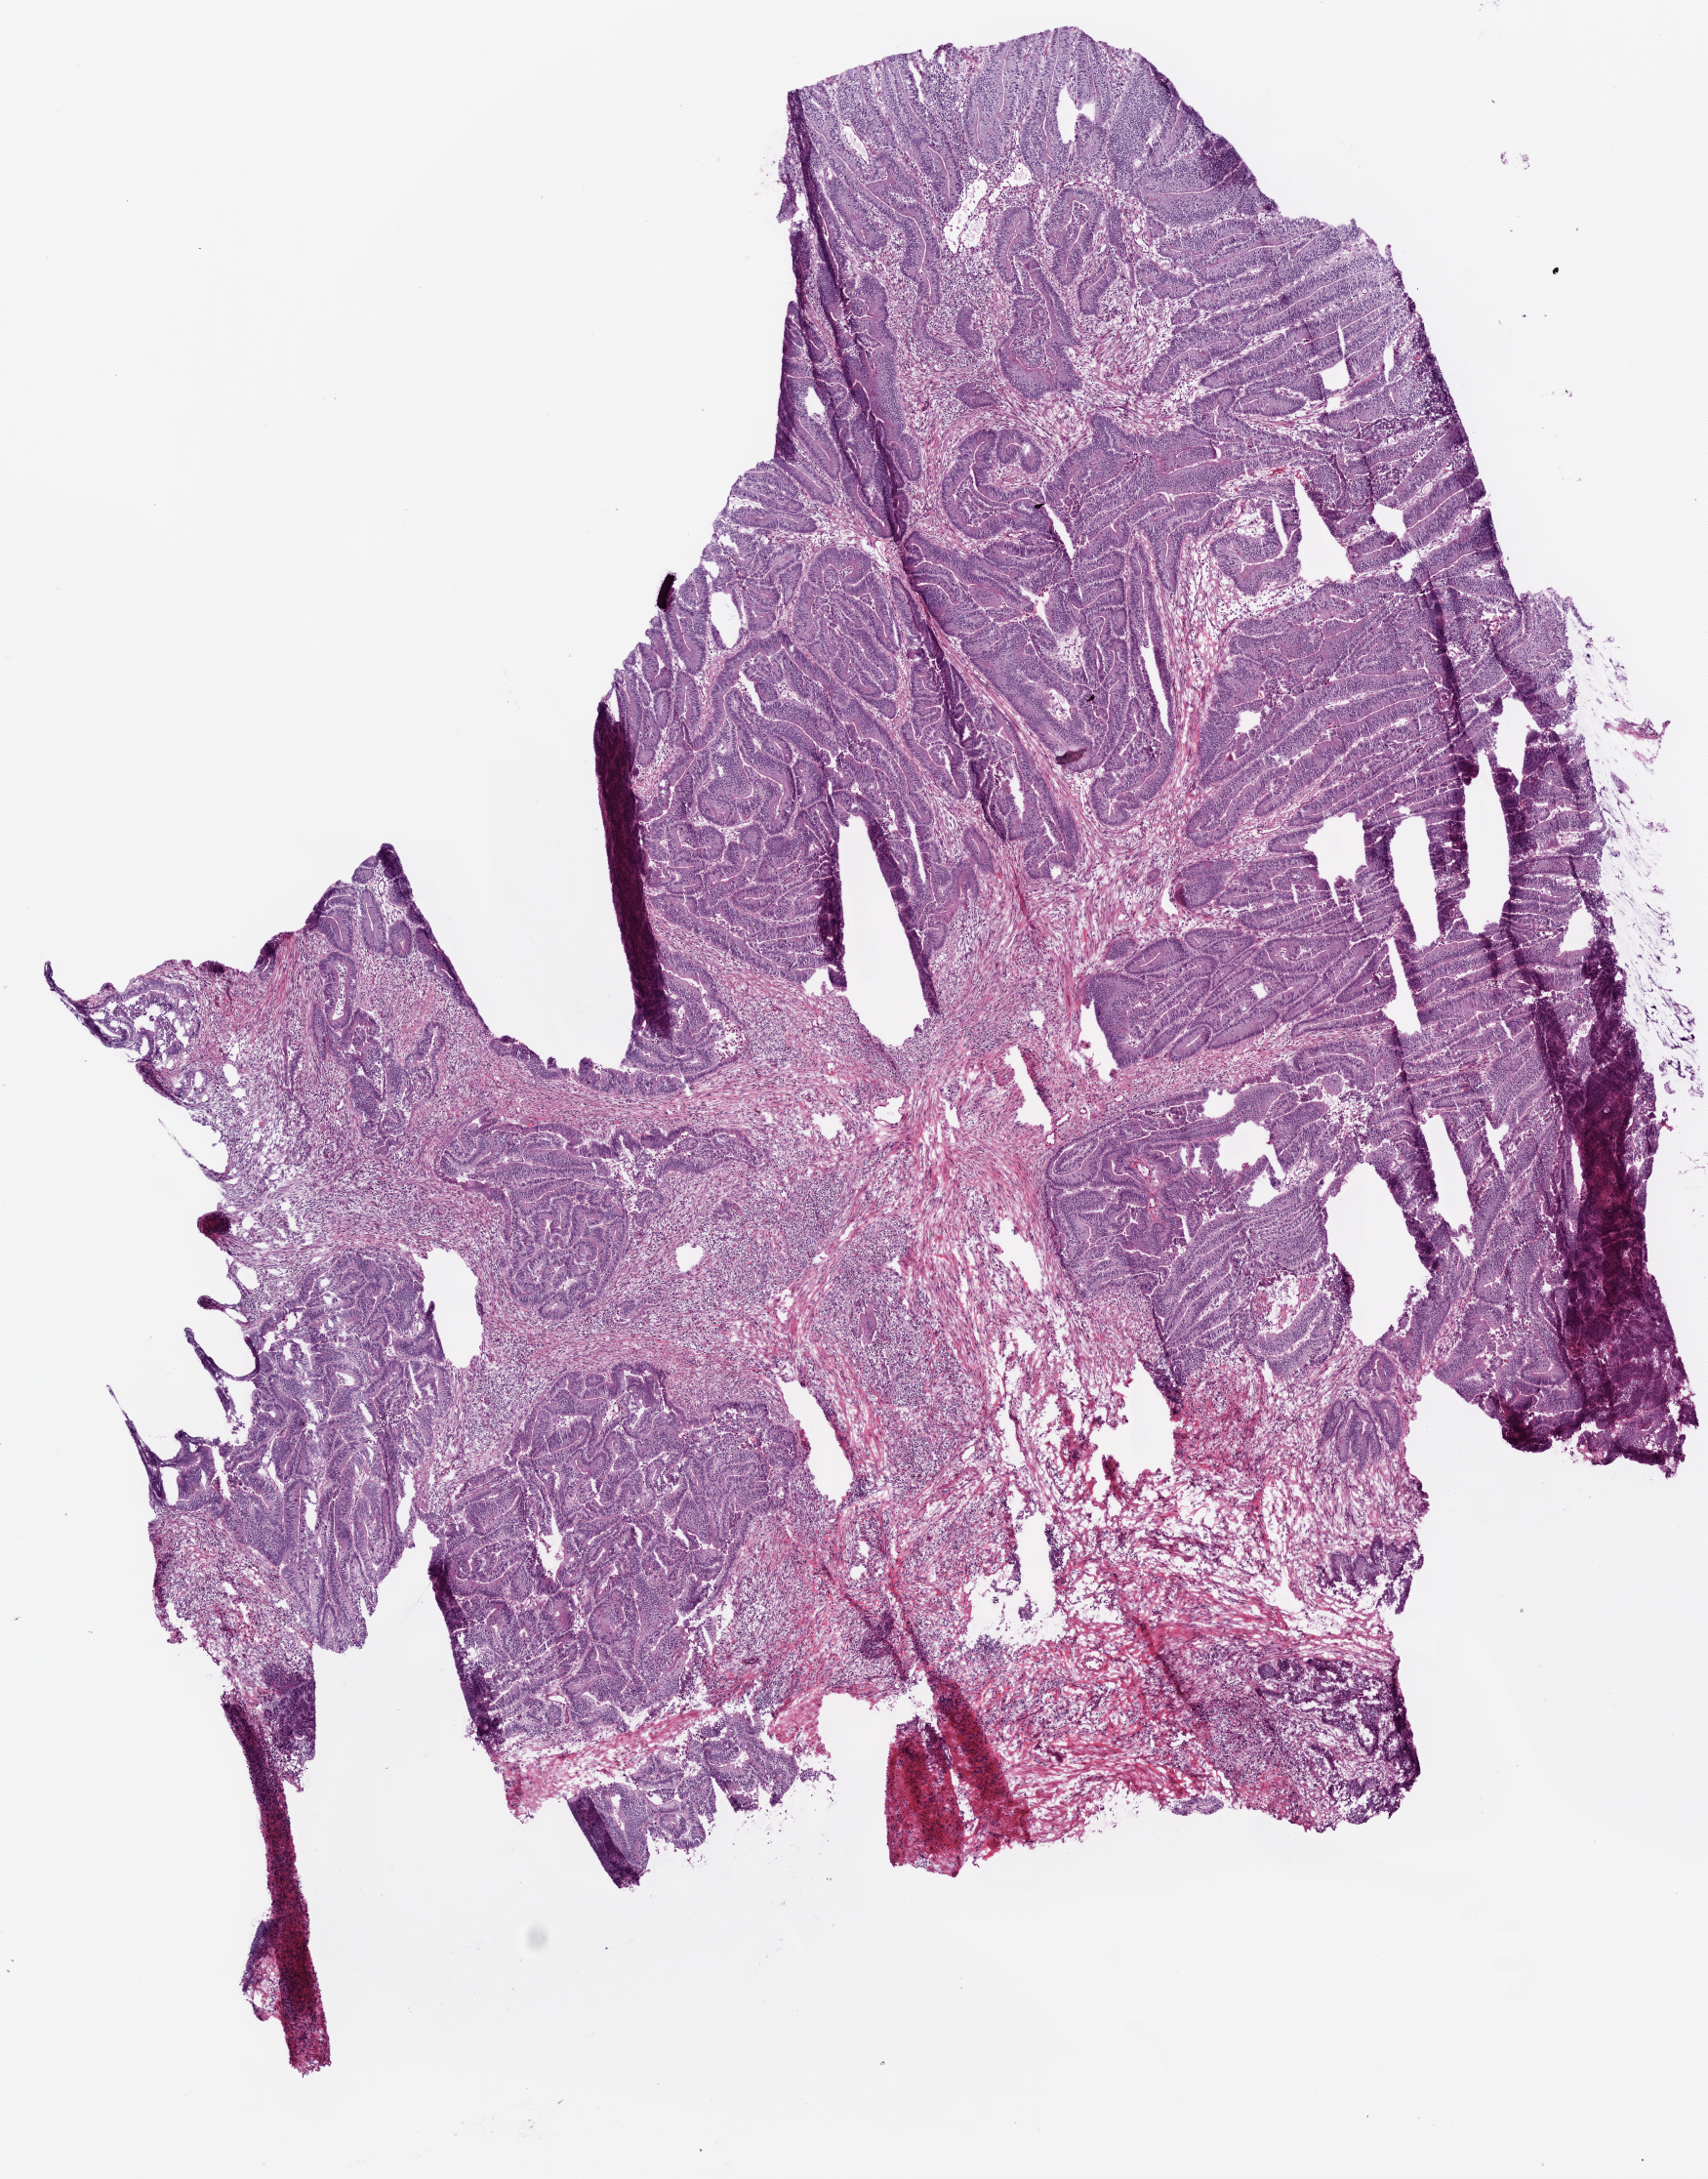
H&E-stained whole-slide image, whole scanned area (about 7.0 x 9.0 mm, slide scanned at 20x) shown as a low-resolution overview. Frozen section. Colon, primary tumour sample. Patient: male, age at initial diagnosis 84 years.
Histologic diagnosis: Adenocarcinoma, NOS (ascending colon).